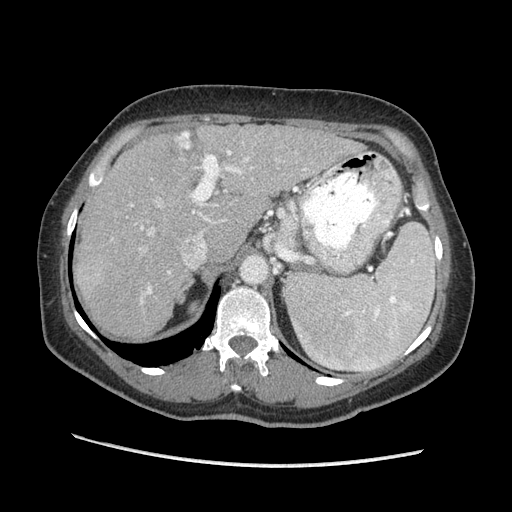
Contrast-enhanced abdominal CT (liver protocol), one axial slice; position 138 of 170 along the scan axis; reconstruction kernel STANDARD; soft-tissue window (W 400 / L 40 HU); 2.5 mm slice thickness; 512 × 512 image matrix, field of view 360 × 360 mm. Case-level facts recorded for this patient, not image findings: diagnosis: hepatocellular carcinoma (patient treated with transarterial chemoembolisation; whether this scan precedes or follows treatment is not stated here); TNM stage (as recorded): Stage-II; Child-Pugh class: A; tumour nodularity: multinodular; tumour size: 4 cm.
Annotated regions visible in this slice (semi-automatically segmented with operator editing):
- liver parenchyma outside the tumour (the mass and vessels are separate outlines, so this box may not span the whole liver): bounding box [x1, y1, x2, y2] px = [75, 124, 364, 340]
- mass: [172, 128, 204, 155]
- liver vessels: [100, 150, 307, 304]